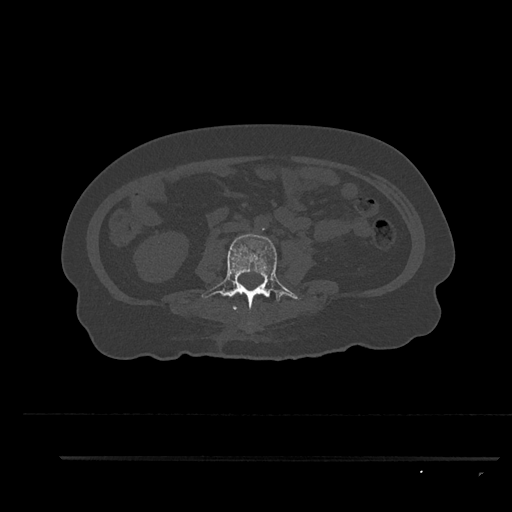
CT including the spine, one axial slice. Position 91 of 797 along the scan axis. Reconstruction kernel Br40s/3. 120 kVp. Bone window (W 1800 / L 400 HU). 0.5 mm slice thickness. 512 × 512 image matrix, field of view 408 × 408 mm. Female patient, age 44 years. From the clinical record (not read from this slice): primary cancer: renal; vertebrae with lytic lesions (as recorded): L1.
Outlined on this slice (semi-automatic segmentation, software-assisted and operator-edited):
- L2 vertebra: box from (x=233, y=306) to (x=237, y=310) px
- L3 vertebra: (x=202, y=234)–(x=301, y=313)